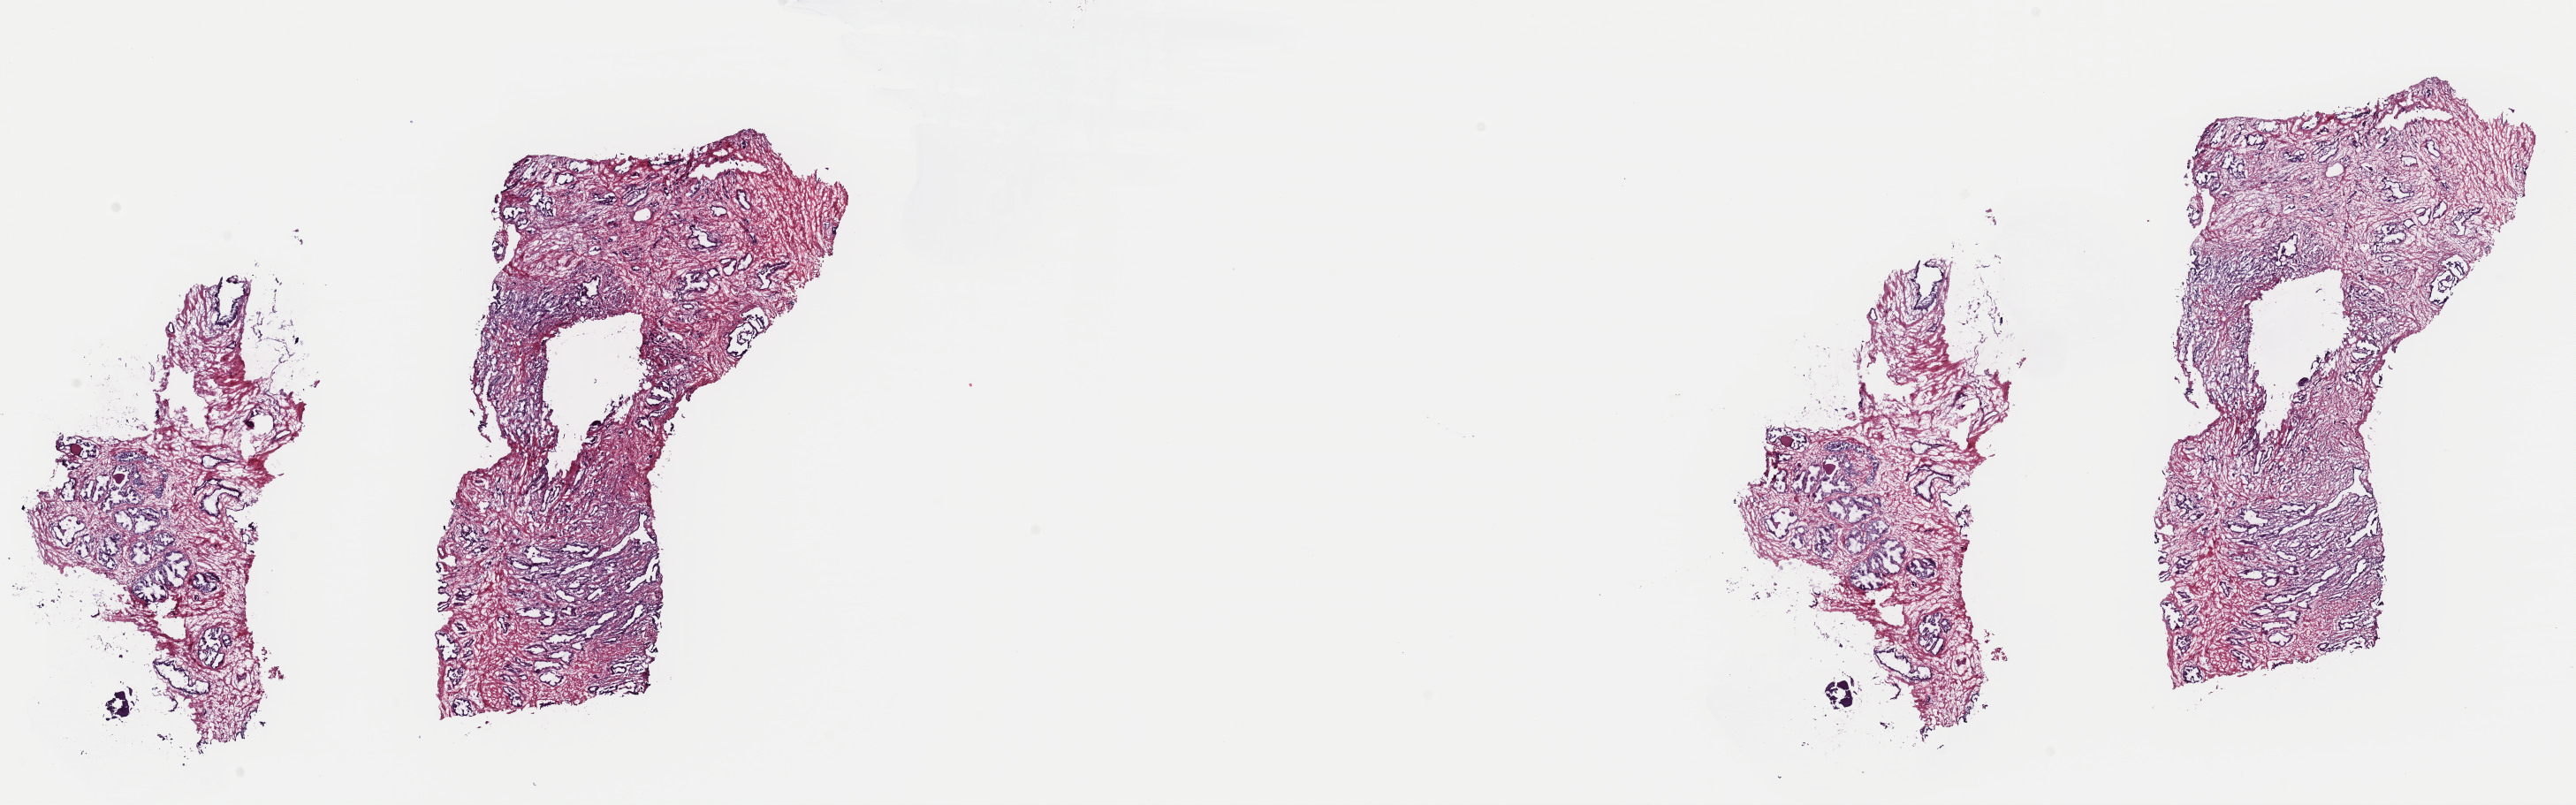
Whole-slide histology image, Hematoxylin and eosin (H&E) stained — low-resolution overview of the scanned area, about 23.0 x 7.2 mm (from a 40x scan), frozen section from the top of the tissue portion, prostate, primary tumour sample. Male, age 55 years at initial diagnosis. Gleason score: 7 (4+3). Slide review estimates, as recorded: tumour cells 70%, tumour nuclei 80%, normal cells 10%, stromal cells 20%, necrosis 0%. Inflammatory infiltration, as recorded: lymphocyte infiltration 0%, monocyte infiltration 0%, neutrophil infiltration 0%.
• diagnosis: Adenocarcinoma, NOS (prostate gland)